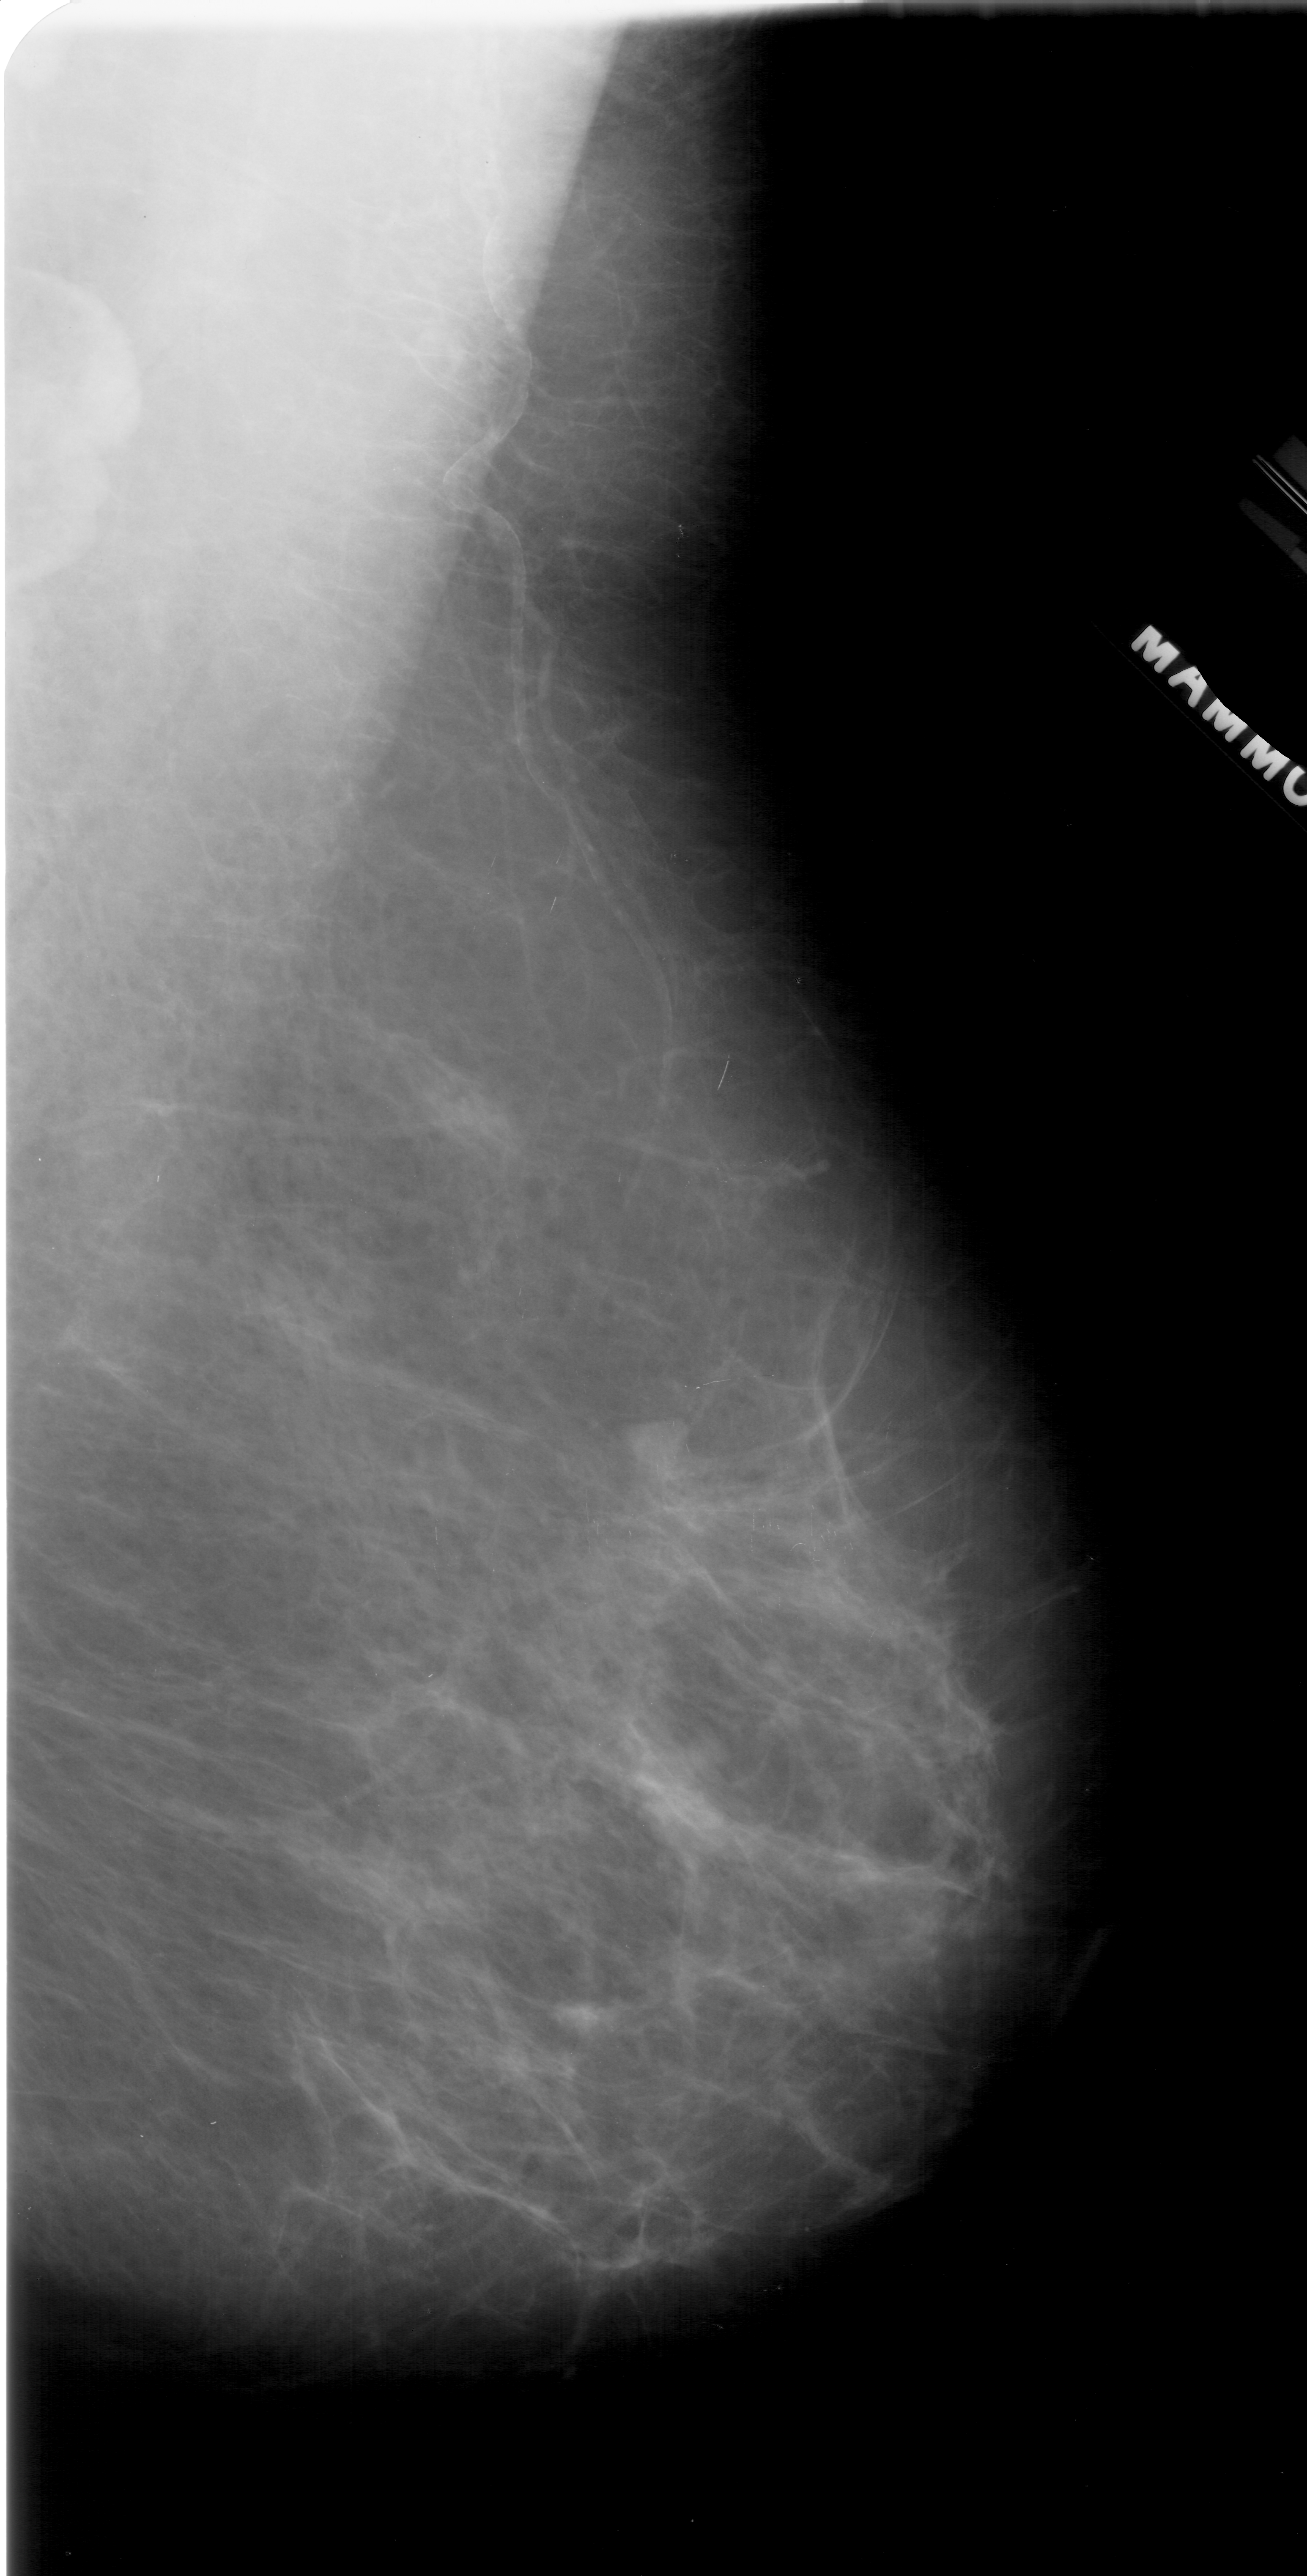
Digitized screen-film mammogram. Right breast. Mediolateral oblique (MLO) view. BI-RADS breast density category 2 (scale 1–4). 1307 × 2576 image matrix.
Expert-marked regions of interest on this image (one box per marked abnormality):
- mass, shape lobulated, margins obscured; BI-RADS assessment category 4; pathology result (as recorded, not read from the image): malignant: bounding box <620,1416,692,1486> (left, top, right, bottom; pixels)